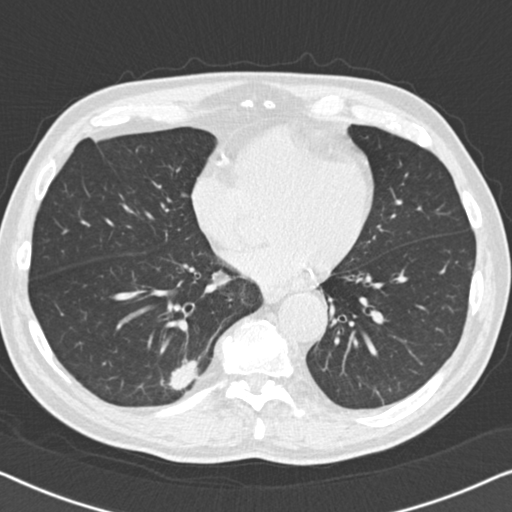
Low-dose screening chest CT, axial slice, second annual screen, lung window (W 1500 / L -600 HU), 2 mm slice thickness, standard (soft-tissue) reconstruction kernel (B30f), 512 × 512 image matrix, field of view 330 × 330 mm. Male, age 74 years at enrolment.
Expert-annotated lung lesion, box from (x=149, y=344) to (x=218, y=407) px. The screening reader recorded 5 non-calcified nodules or masses ≥4 mm on this exam (right lower lobe, right lower lobe, right lower lobe, left lower lobe, left lower lobe); which of them this box marks is not recorded. Official screen result: positive, other. Participant outcome: lung cancer diagnosed 55 days after this screen — bronchiolo-alveolar adenocarcinoma, NOS, right lower lobe, moderately differentiated (G2), stage IA (AJCC 6th edition), 16 mm at pathology.